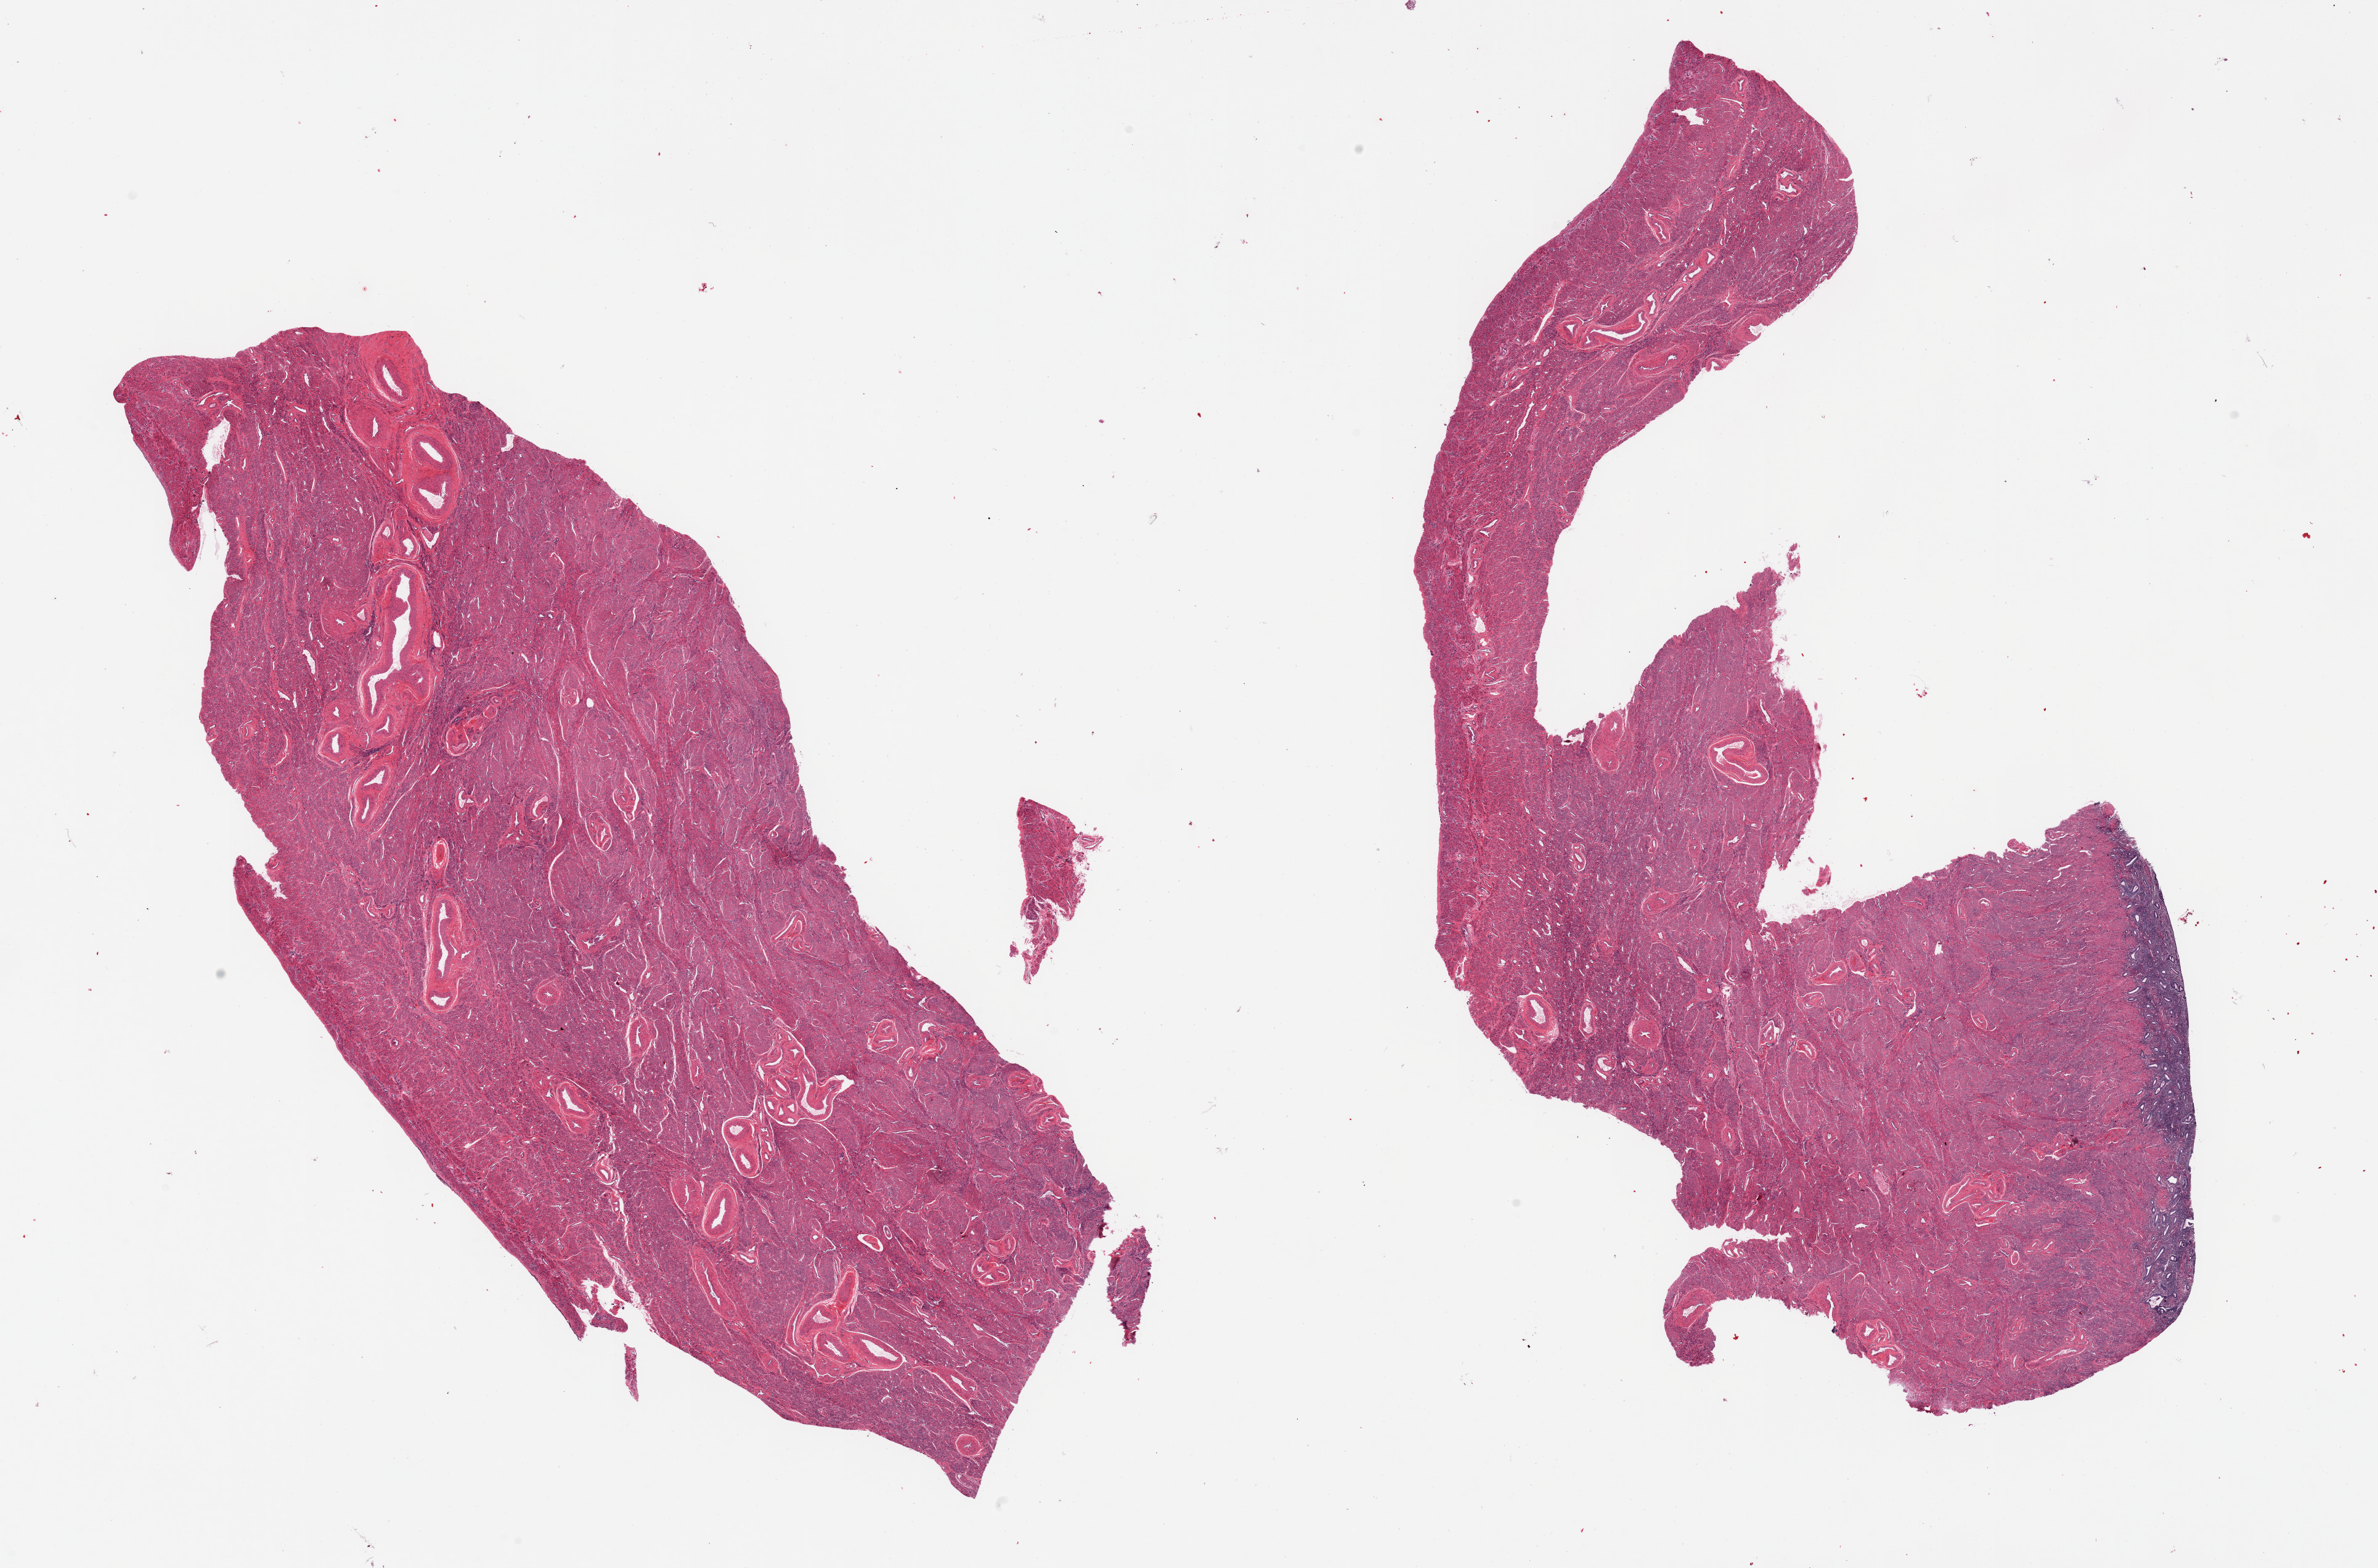
Hematoxylin and eosin (H&E) whole-slide image, brightfield — shown as a low-resolution overview of the whole scanned area (about 30.5 x 20.1 mm); PAXgene-fixed, paraffin-embedded tissue; target tissue: uterus; tissue donor sample.
Reviewer comment on this tissue sample: 2 pieces, one piece contains endometrium and one piece myometrium only.